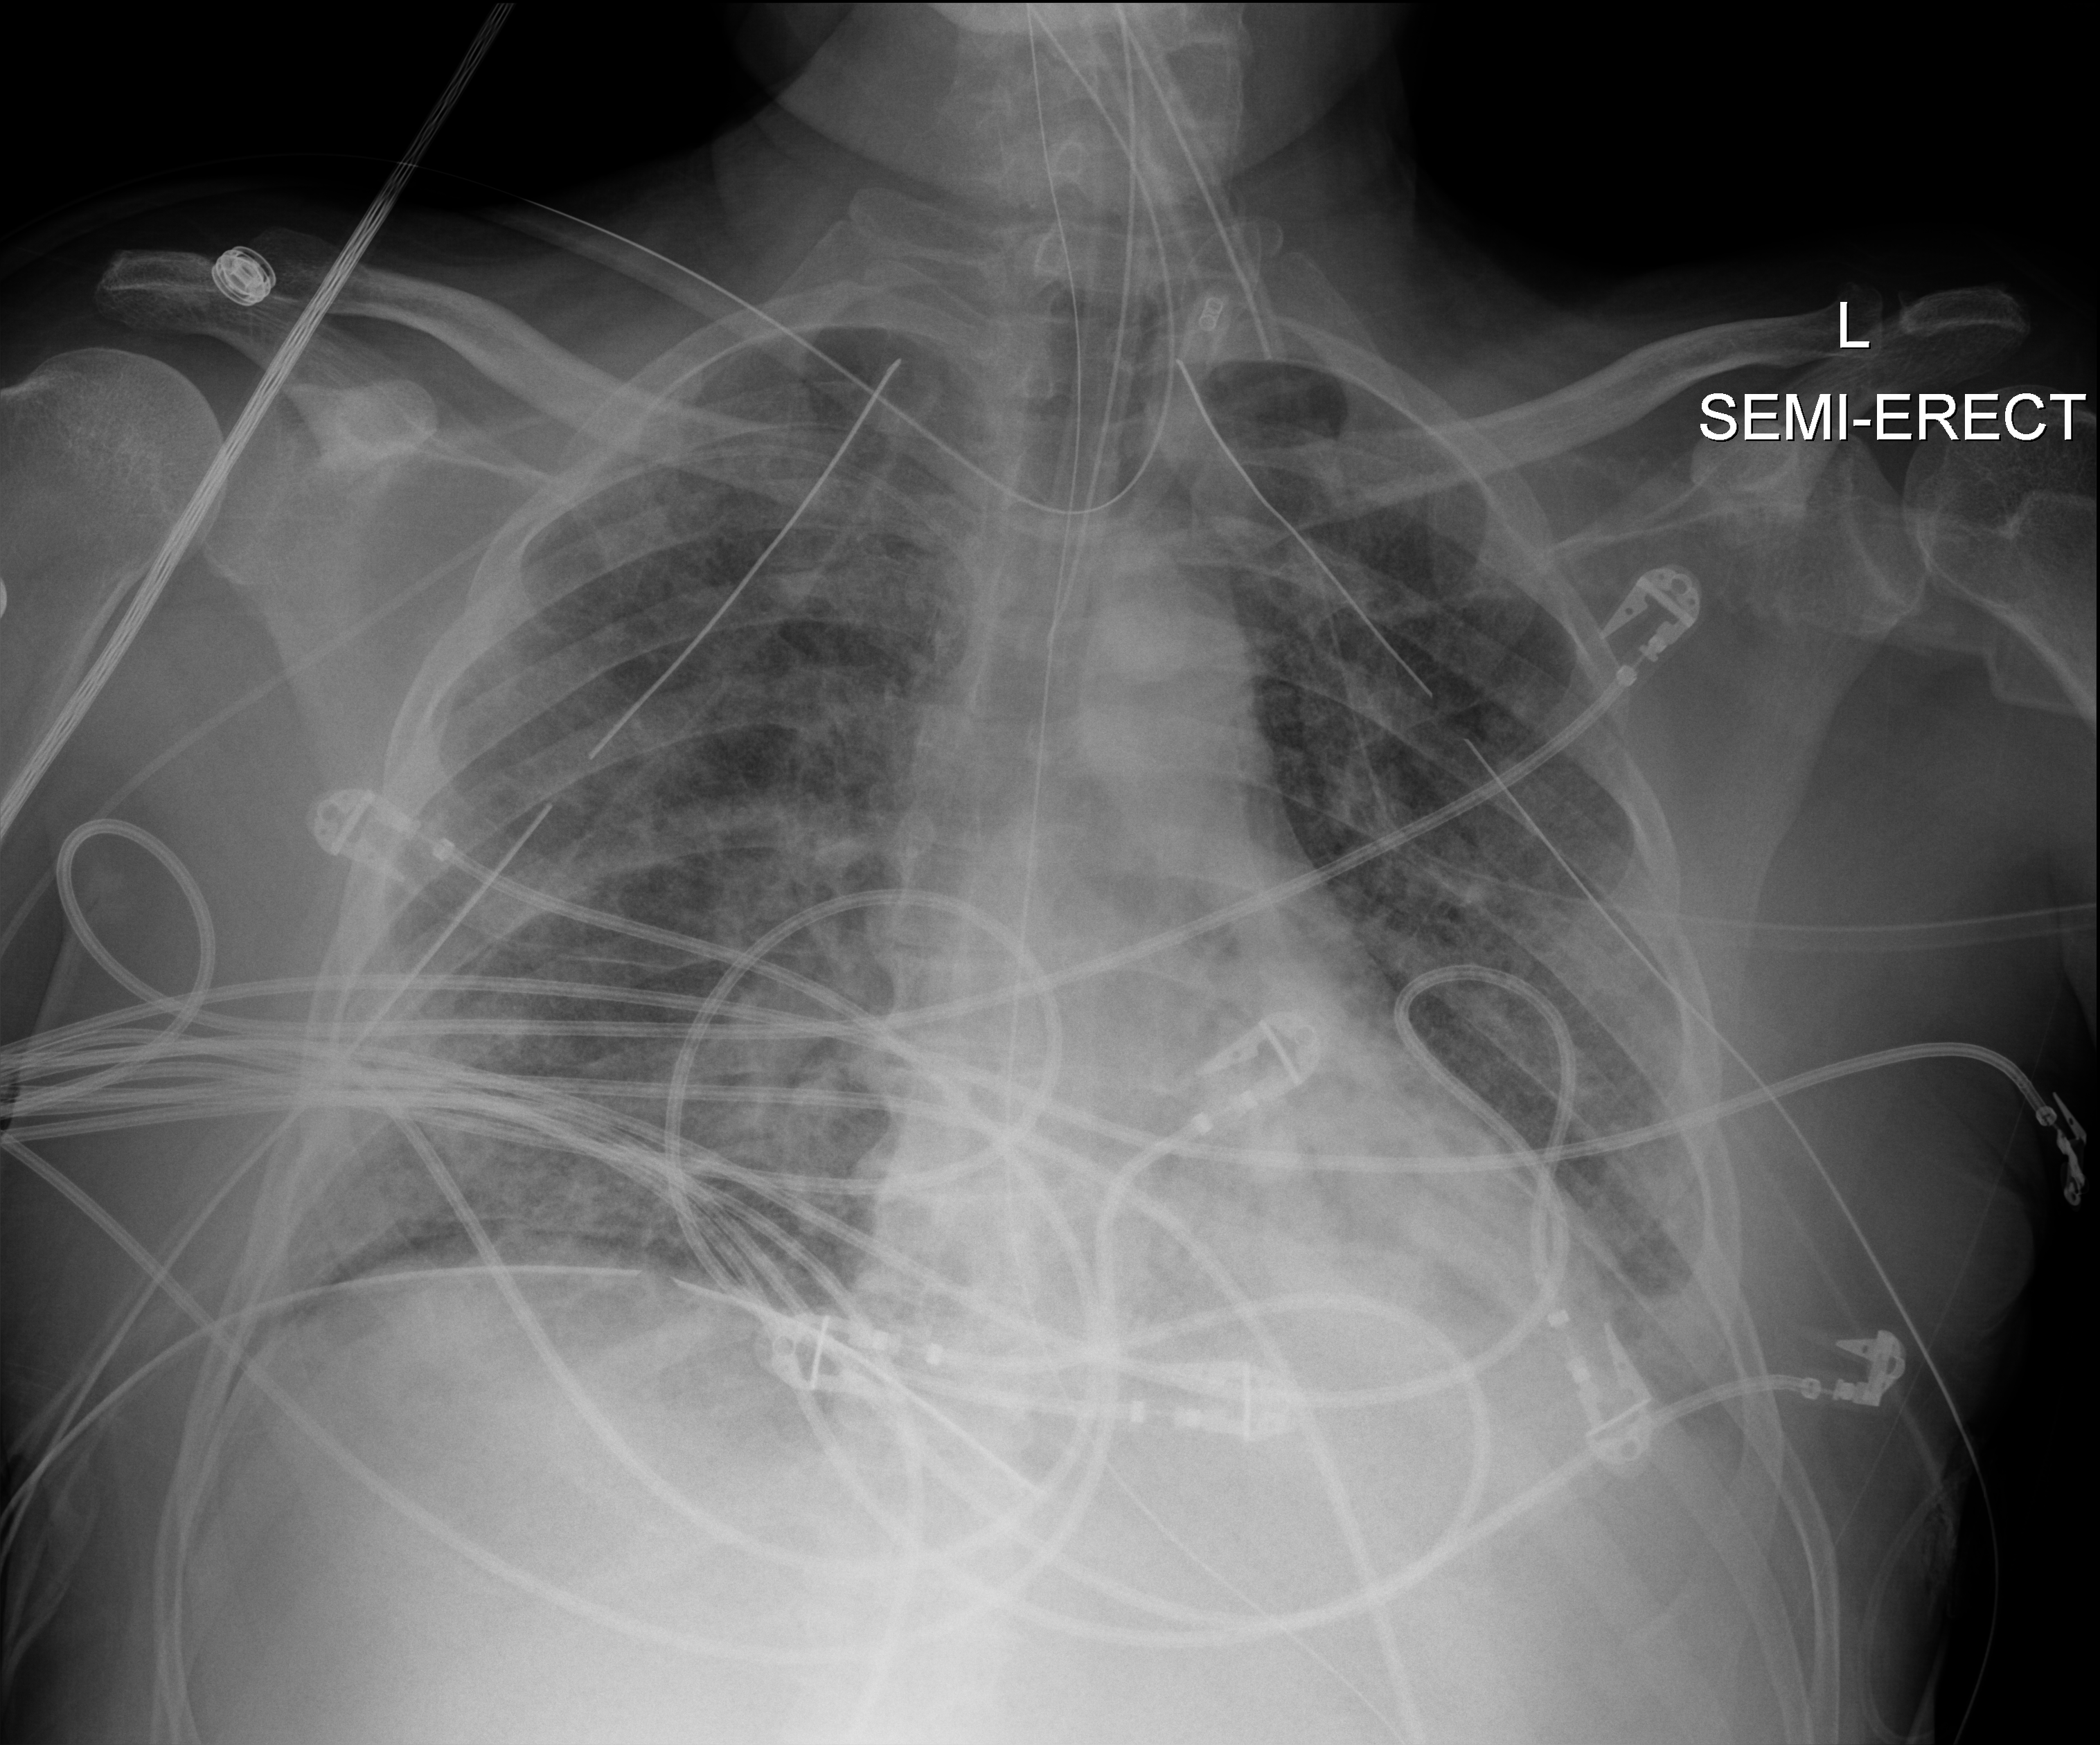
Chest X-ray (portable). Patient hospitalised with COVID-19; male, aged 18–59 years.
Admission-level facts for this patient (not findings on this image; timing relative to this image not recorded):
- mechanically ventilated during this hospital stay: yes
- admitted to intensive care during this hospital stay: yes